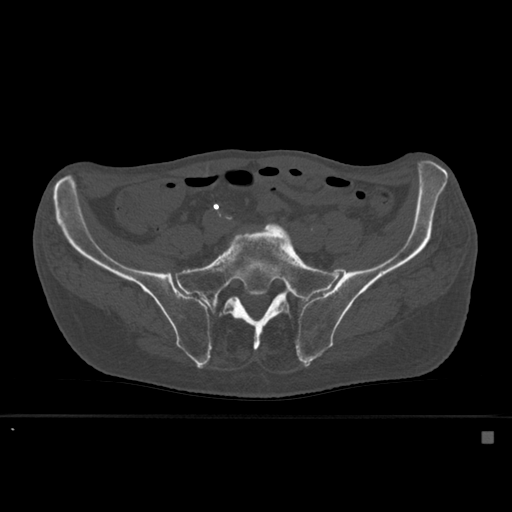
CT including the spine, one axial slice. Position 158 of 527 along the scan axis. Bone window (W 1800 / L 400 HU). 512 × 512 image matrix. Patient: male, 78 years. From the clinical record (not read from this slice): primary cancer: prostate.
Annotated regions visible in this slice (semi-automatically segmented with operator editing):
- L5 vertebra: bounding box (x1, y1, x2, y2) in pixels: (279, 302, 289, 312)